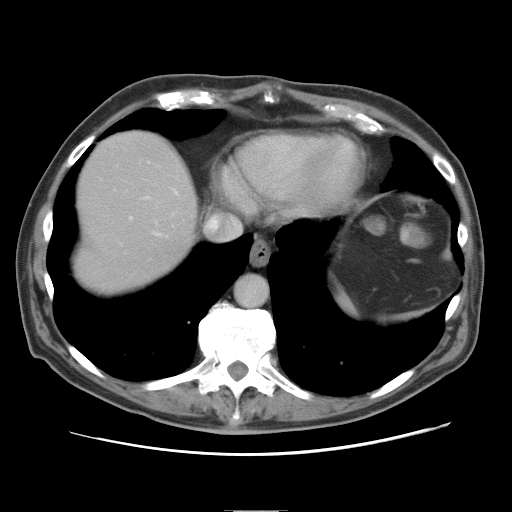
Contrast-enhanced abdominal CT, one axial slice. Position 71 of 89 along the scan axis. Intravenous contrast given. Soft-tissue window (W 400 / L 40 HU). 5 mm slice thickness. 512 × 512 image matrix. Male patient, age 69 years. Case-level facts recorded for this patient, not image findings: diagnosis: colorectal cancer liver metastases, imaged before liver resection; multiple liver metastases: no; largest metastasis: 8.5 cm; disease in both lobes: no.
Annotated regions visible in this slice (manually delineated by an expert):
- hepatic veins: bounding box [x1, y1, x2, y2] px = [141, 187, 240, 240]
- liver: [74, 132, 197, 292]
- planned liver remnant (the part of the liver to remain after resection): [74, 133, 197, 292]
- portal vein (with intrahepatic branches): [130, 216, 133, 220]